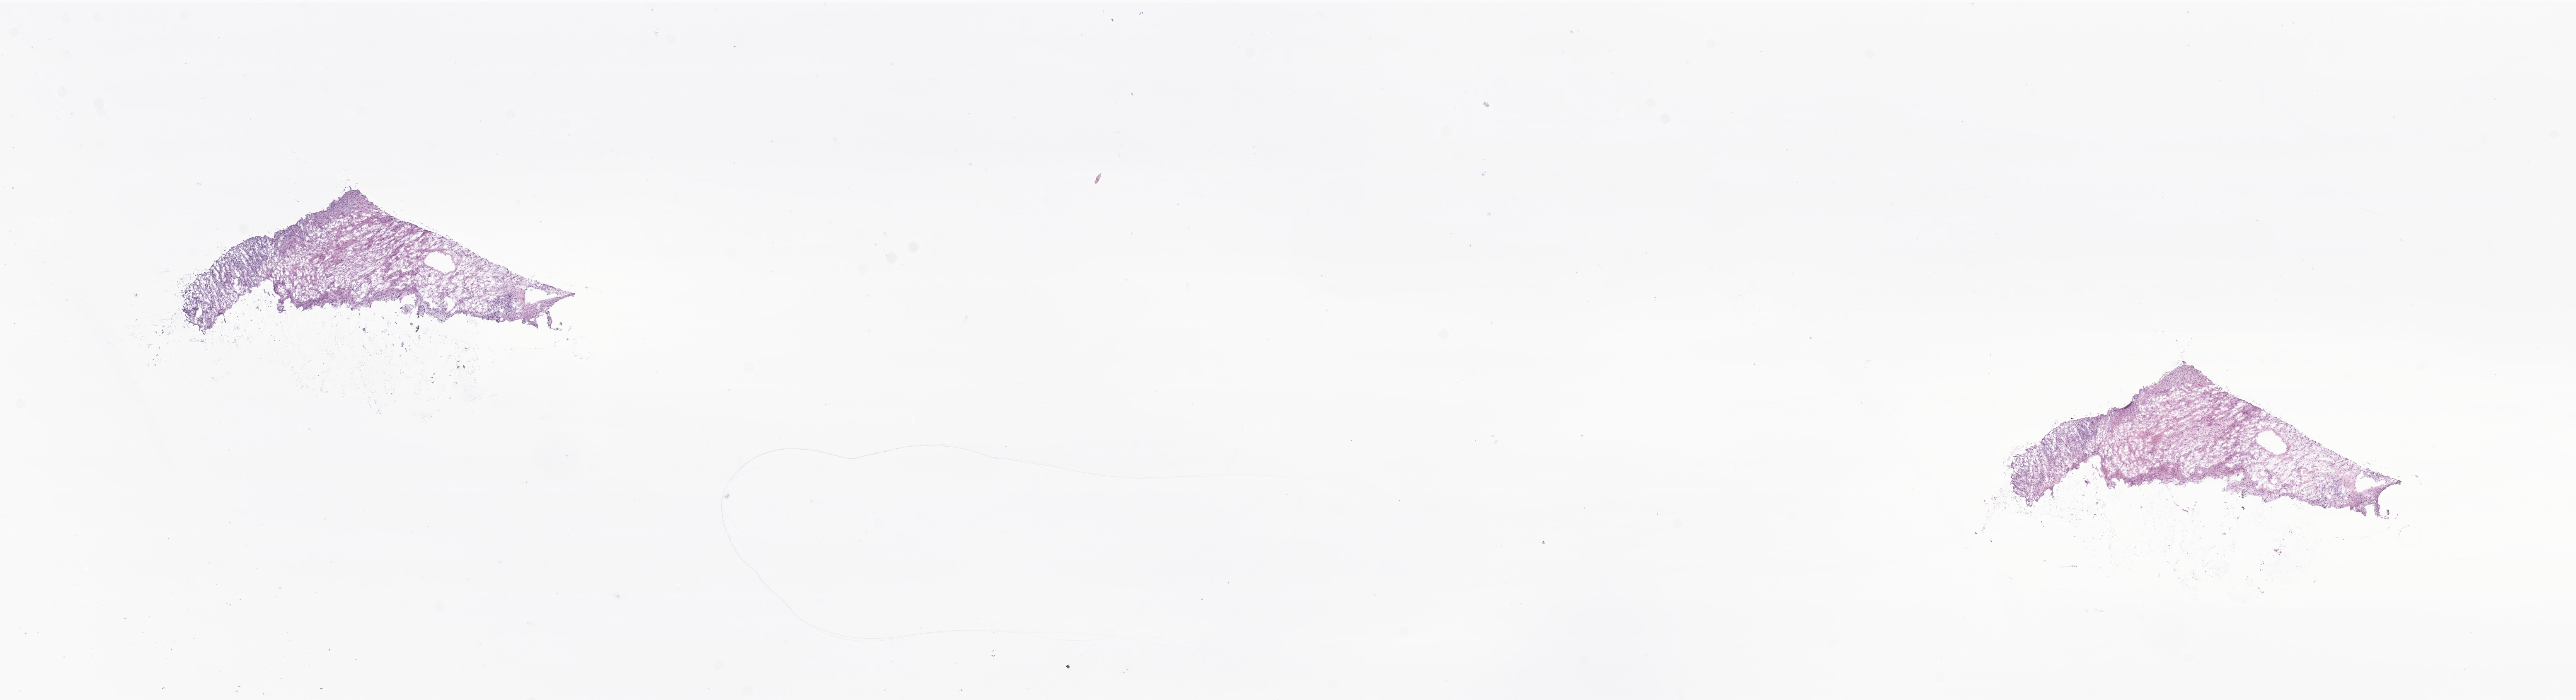
Hematoxylin and eosin (H&E) whole-slide image of tumor tissue from the testis, whole scanned area (about 26.2 x 7.1 mm) shown as a low-resolution overview, frozen section (OCT-embedded). Male patient, age 166 months (13 years 10 months).
Recorded diagnosis: Embryonal rhabdomyosarcoma, NOS.